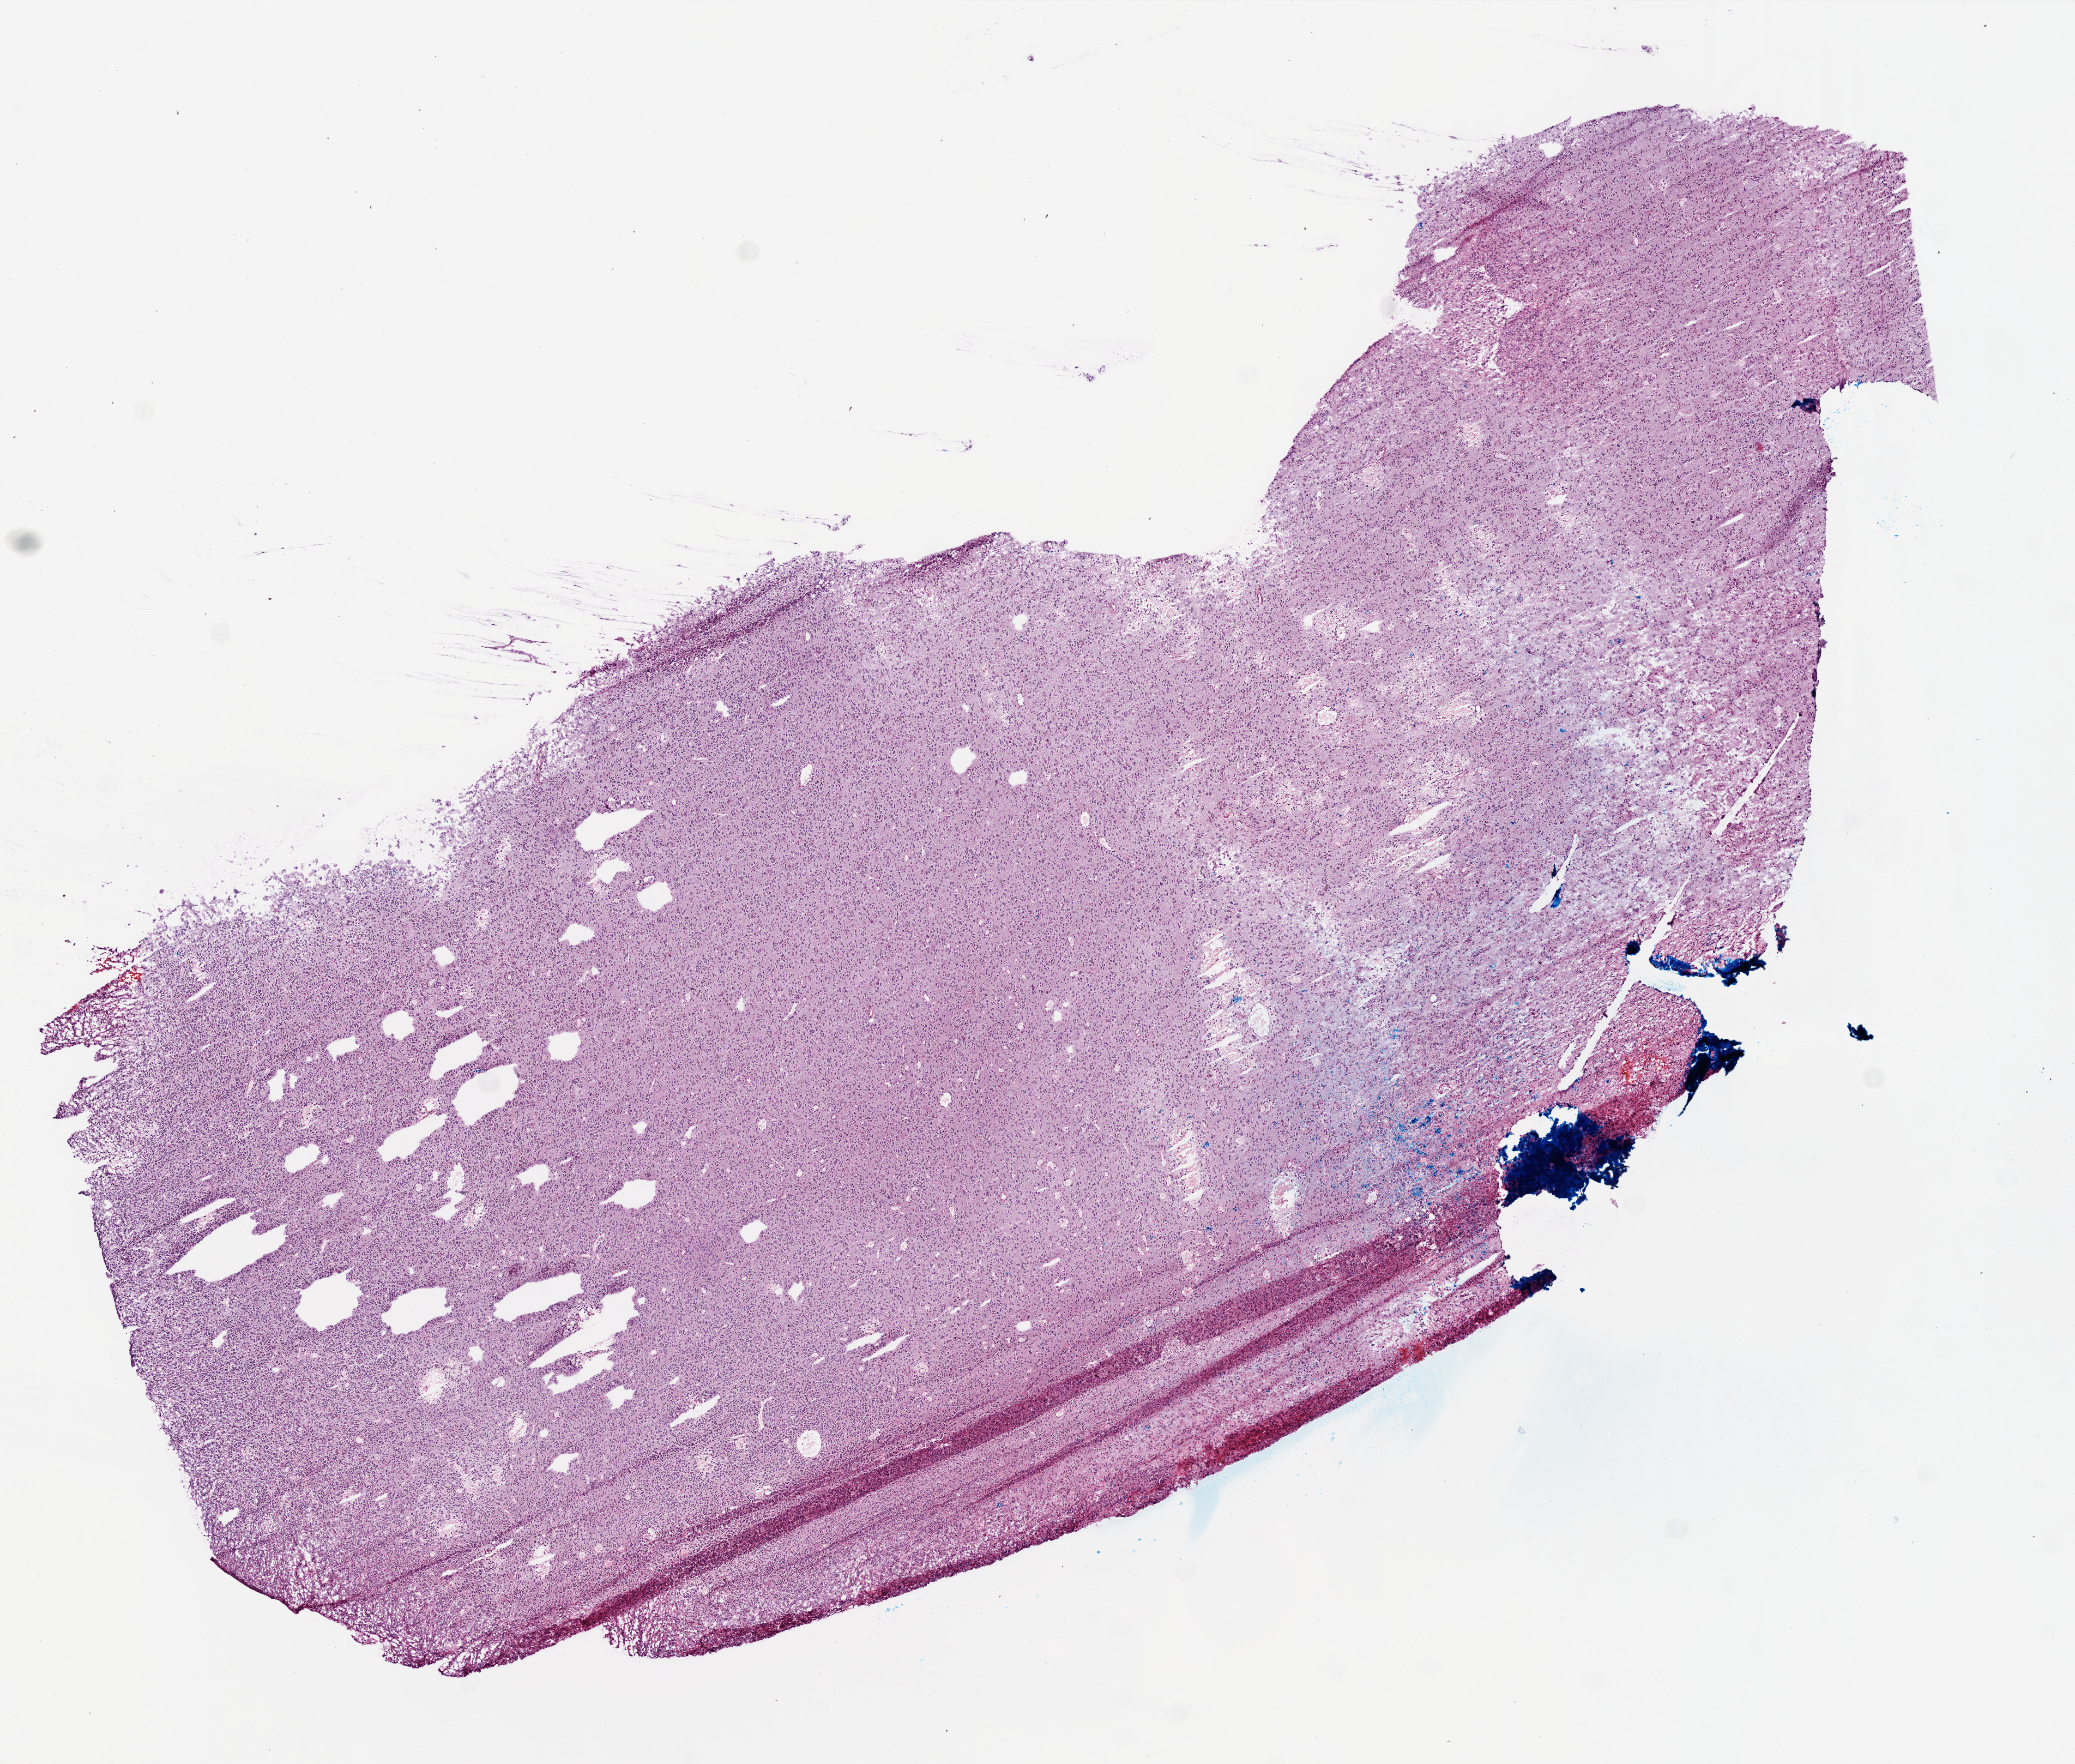
Whole-slide histology image, Hematoxylin and eosin (H&E) stained, a low-resolution overview of the entire scanned area, about 9.0 x 7.6 mm. Frozen section. Brain, primary tumour sample. Patient: male, age at initial diagnosis 59 years. Slide review estimates, as recorded: tumour cells 80%, tumour nuclei 95%, normal cells 0%, stromal cells 20%, necrosis 0%.
• diagnosis: Glioblastoma